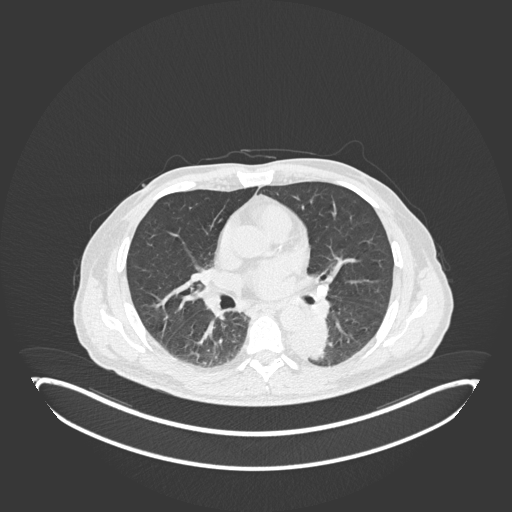
Chest CT, one axial slice. Position 104 of 251 along the scan axis. Reconstruction kernel B30f. Lung window (W 1500 / L -600 HU). 1 mm slice thickness. 512 × 512 image matrix, field of view 500 × 500 mm. Male patient, age 72 years. From the clinical record (not read from this slice): clinical TNM (as recorded): T2b N0 M1.
Structures marked on this image (rectangle marked by the reading radiologist):
- lung tumour (recorded histology: adenocarcinoma): bounding box (x1, y1, x2, y2) in pixels: (281, 314, 327, 365)